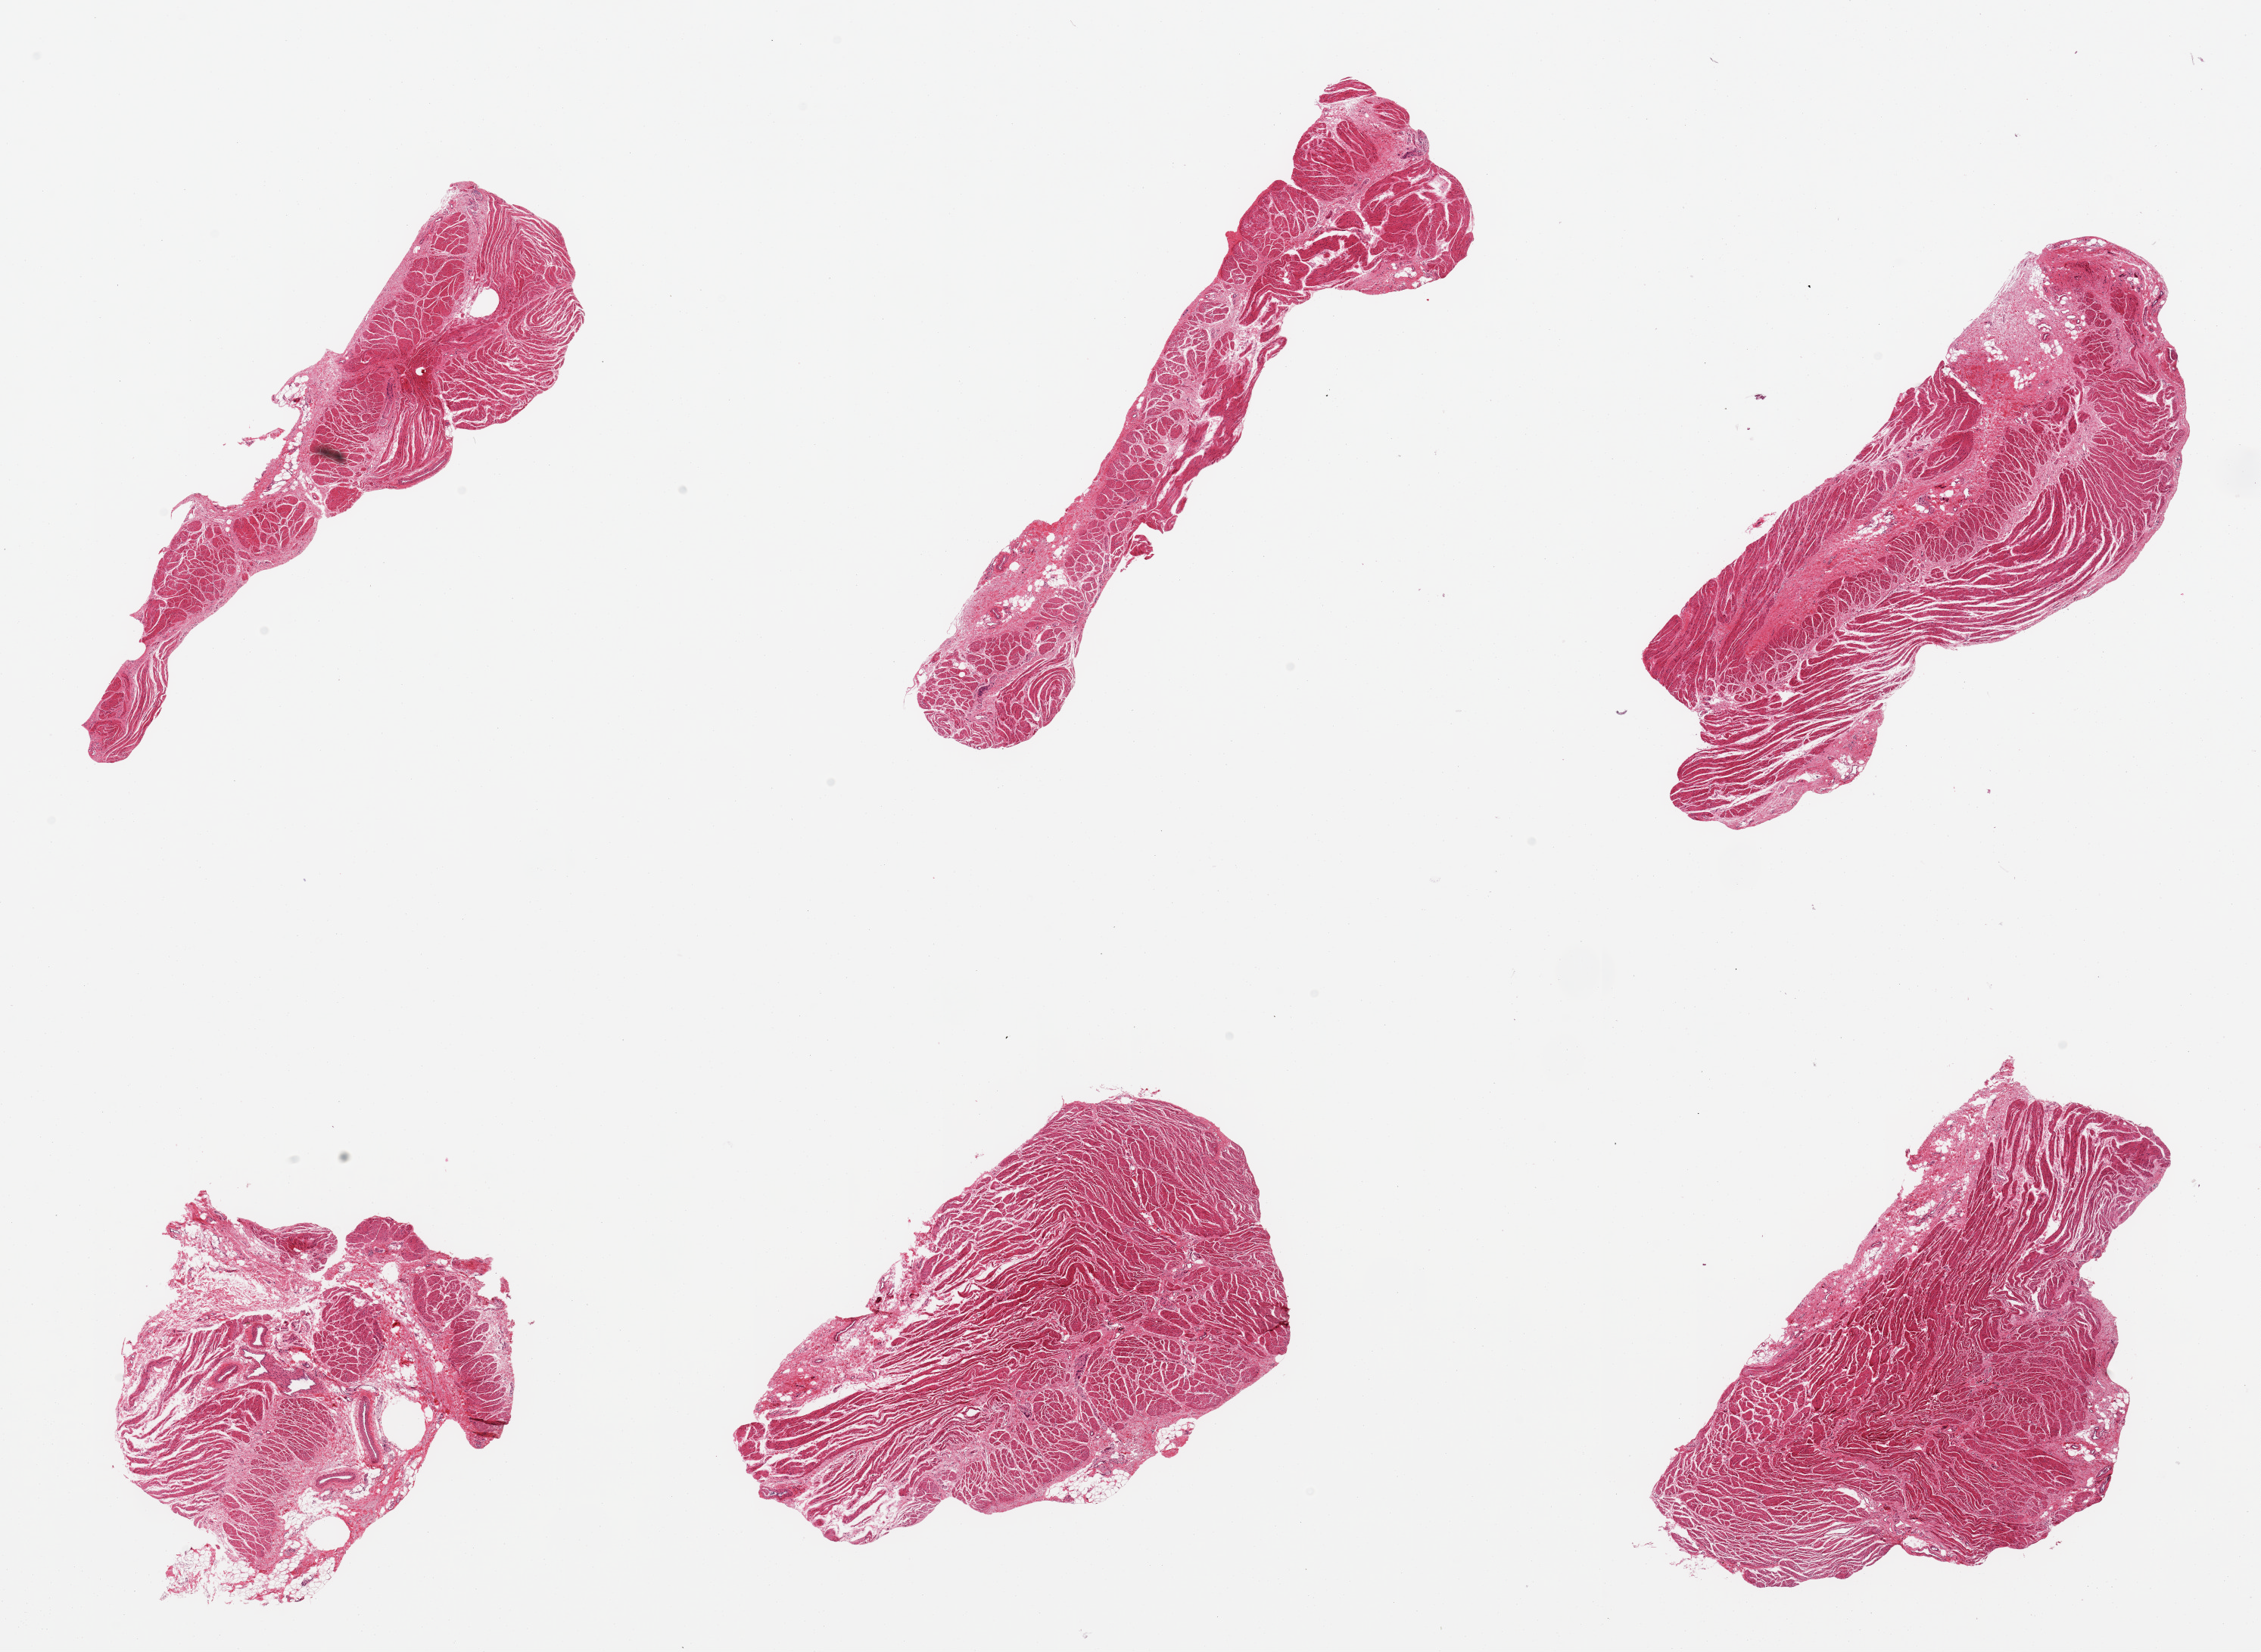
Haematoxylin and eosin whole-slide image, brightfield — shown as a low-resolution overview of the whole scanned area (about 23.6 x 17.3 mm, acquisition: 20x scan), PAXgene-fixed paraffin-embedded (PFPE) section, section of gastroesophageal junction (target tissue), donor tissue sample. Donor sex: female.
Reviewer comment on this tissue sample: 6 pieces; target muscularis with small amounts of attached loose connective tissue.